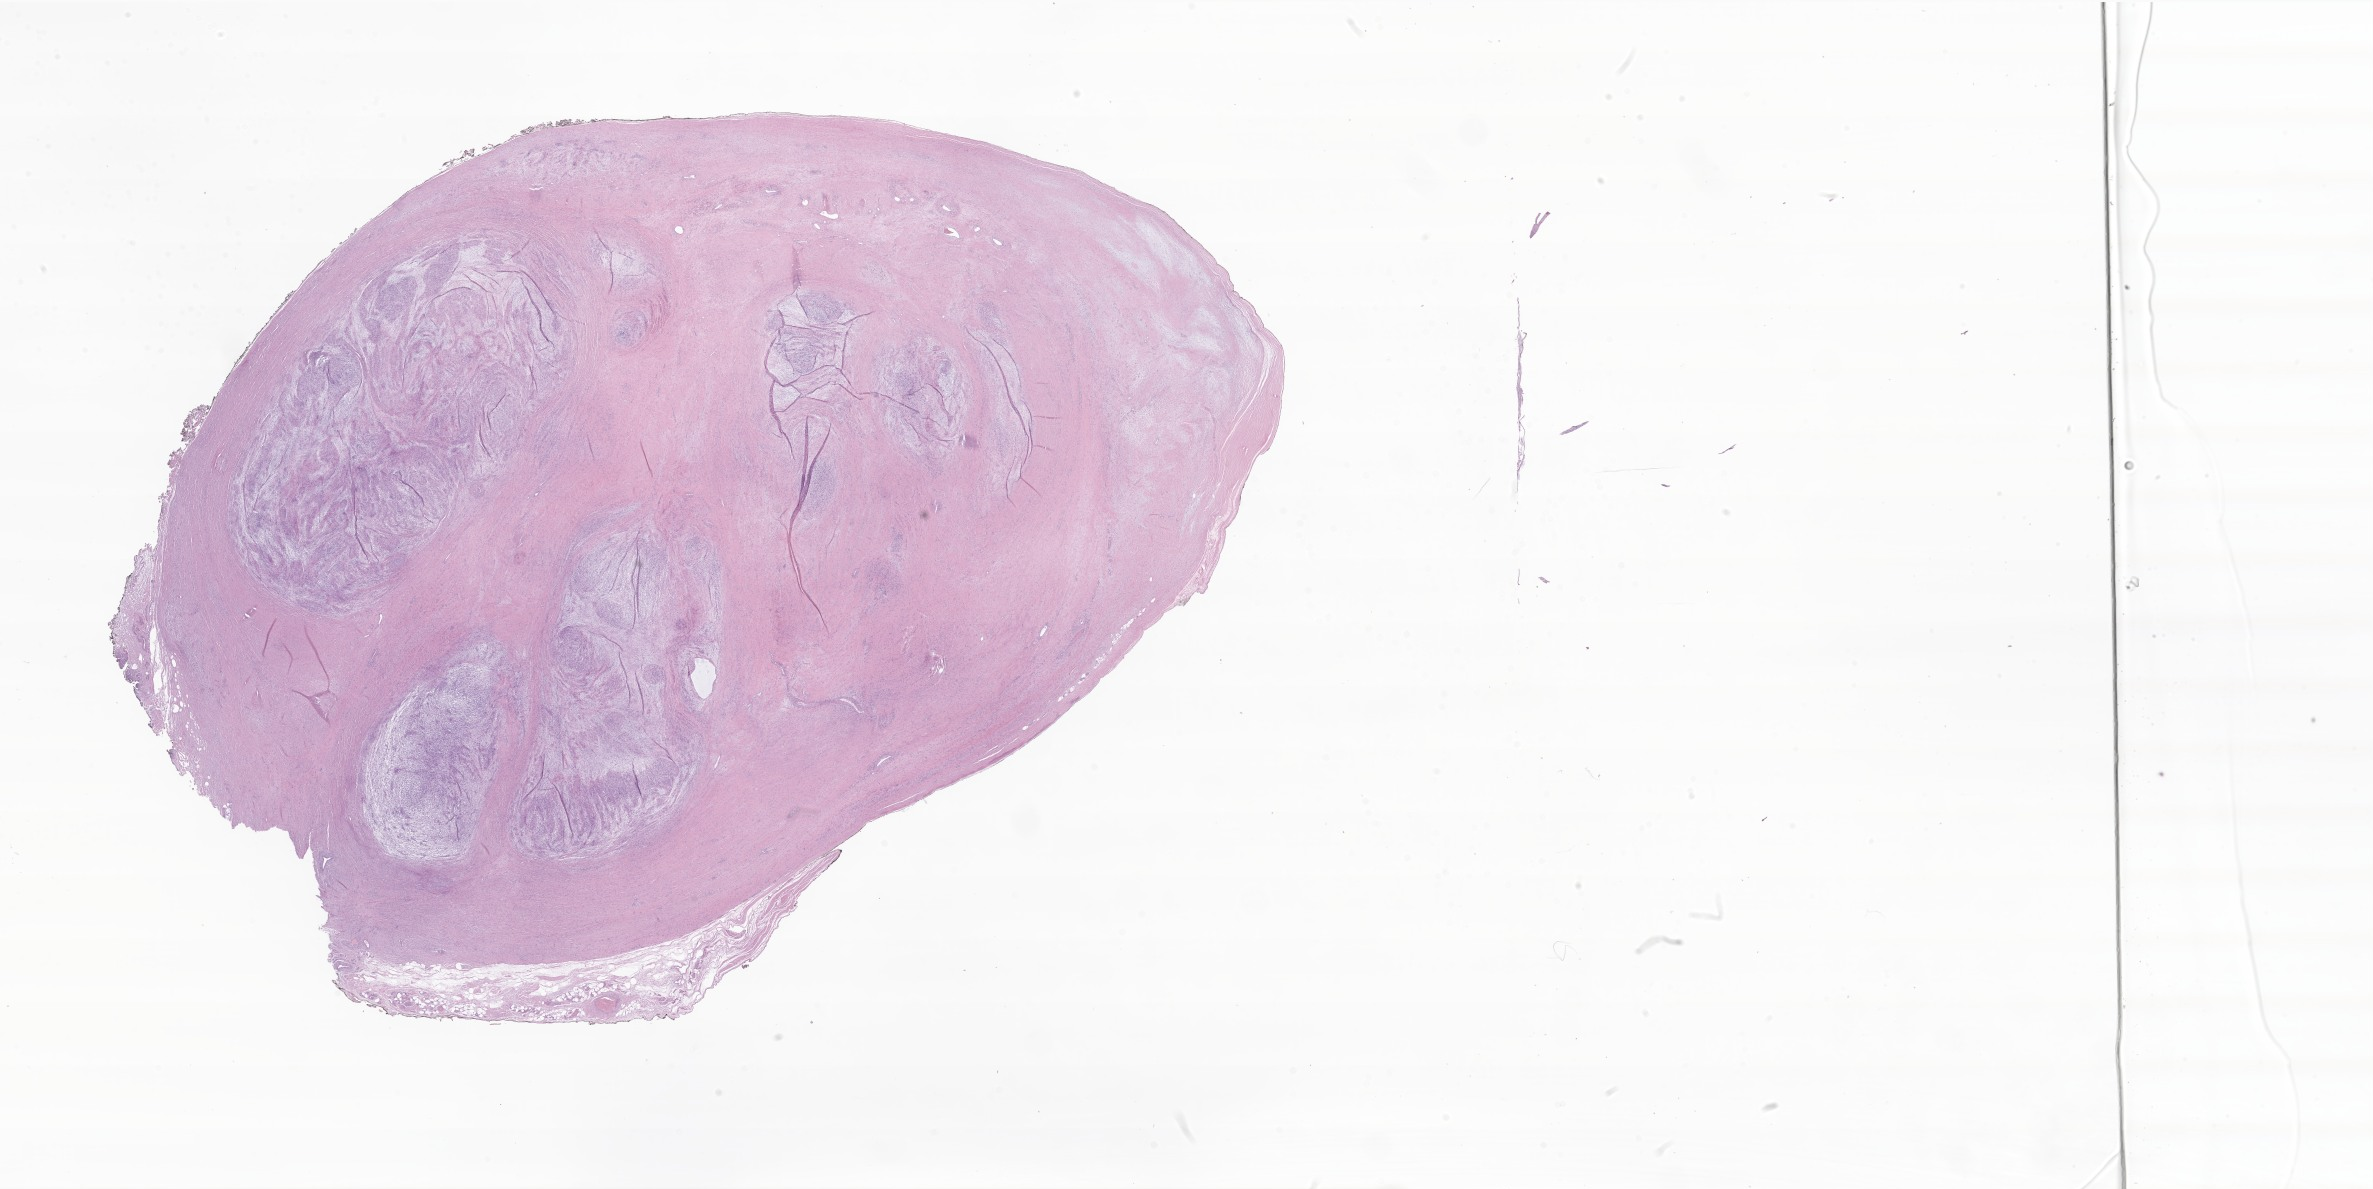
H&E whole-slide image of tumor tissue from the soft tissue of lower extremity, a low-resolution overview of the entire scanned area, about 40.0 x 20.1 mm, FFPE section. Patient: female, age 123 months (10 years 3 months).
* diagnosis (ICD-O-3 morphology term): Myxofibrosarcoma